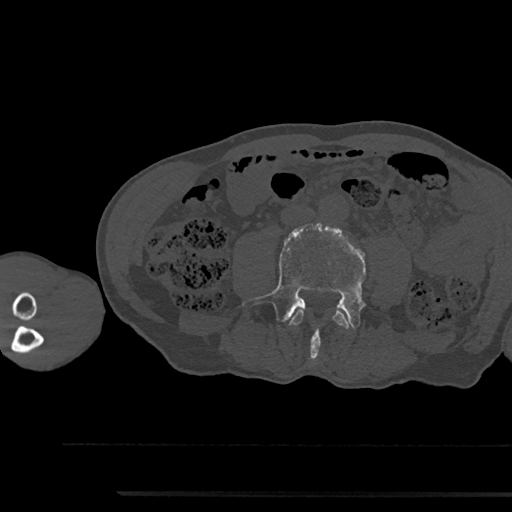
CT including the spine, one axial slice; slice 432 of 797 in the series (ordered by position); reconstruction kernel Br40s/3; 120 kVp; bone window (W 1800 / L 400 HU); 0.5 mm slice thickness; 512 × 512 image matrix. Patient: male, 79 years. From the clinical record (not read from this slice): primary cancer: prostate.
Outlined on this slice (semi-automatic segmentation, software-assisted and operator-edited):
- L3 vertebra: box from (x=290, y=310) to (x=349, y=329) px
- L4 vertebra: (x=243, y=224)–(x=366, y=359)